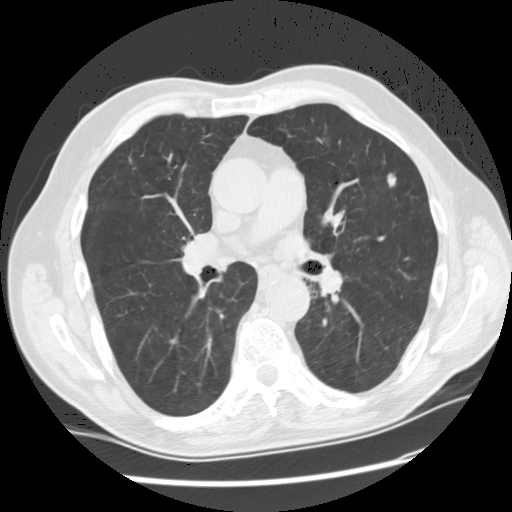
Axial slice from a low-dose chest CT screening exam; third annual screen; lung window (W 1500 / L -600 HU); slice 73 of 159 in the series; 512 × 512 image matrix, field of view 360 × 360 mm. Male, age 71 years at enrolment. Current smoker at enrolment.
• Lesion marked by an expert reader, bounding box <362,162,413,204> (left, top, right, bottom; pixels).
• The screening reader recorded 2 non-calcified nodules or masses ≥4 mm on this exam (lingula, left upper lobe); which of them this box marks is not recorded.
• Official screen result: positive, other.
• Participant outcome: lung cancer diagnosed 100 days after this screen — adenocarcinoma, NOS, left upper lobe, moderately differentiated (G2), stage IA (AJCC 6th edition), 10 mm at pathology.